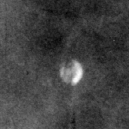
Region of interest cut from a scanned film mammogram (one marked finding); right breast; CC view; BI-RADS breast density category 3 (scale 1–4).
Finding: calcifications, morphology round and regular / lucent centered; BI-RADS assessment category 2; subtlety rating 3 on a 1 (subtle) to 5 (obvious) scale; benign; no additional work-up was recommended (benign without callback).